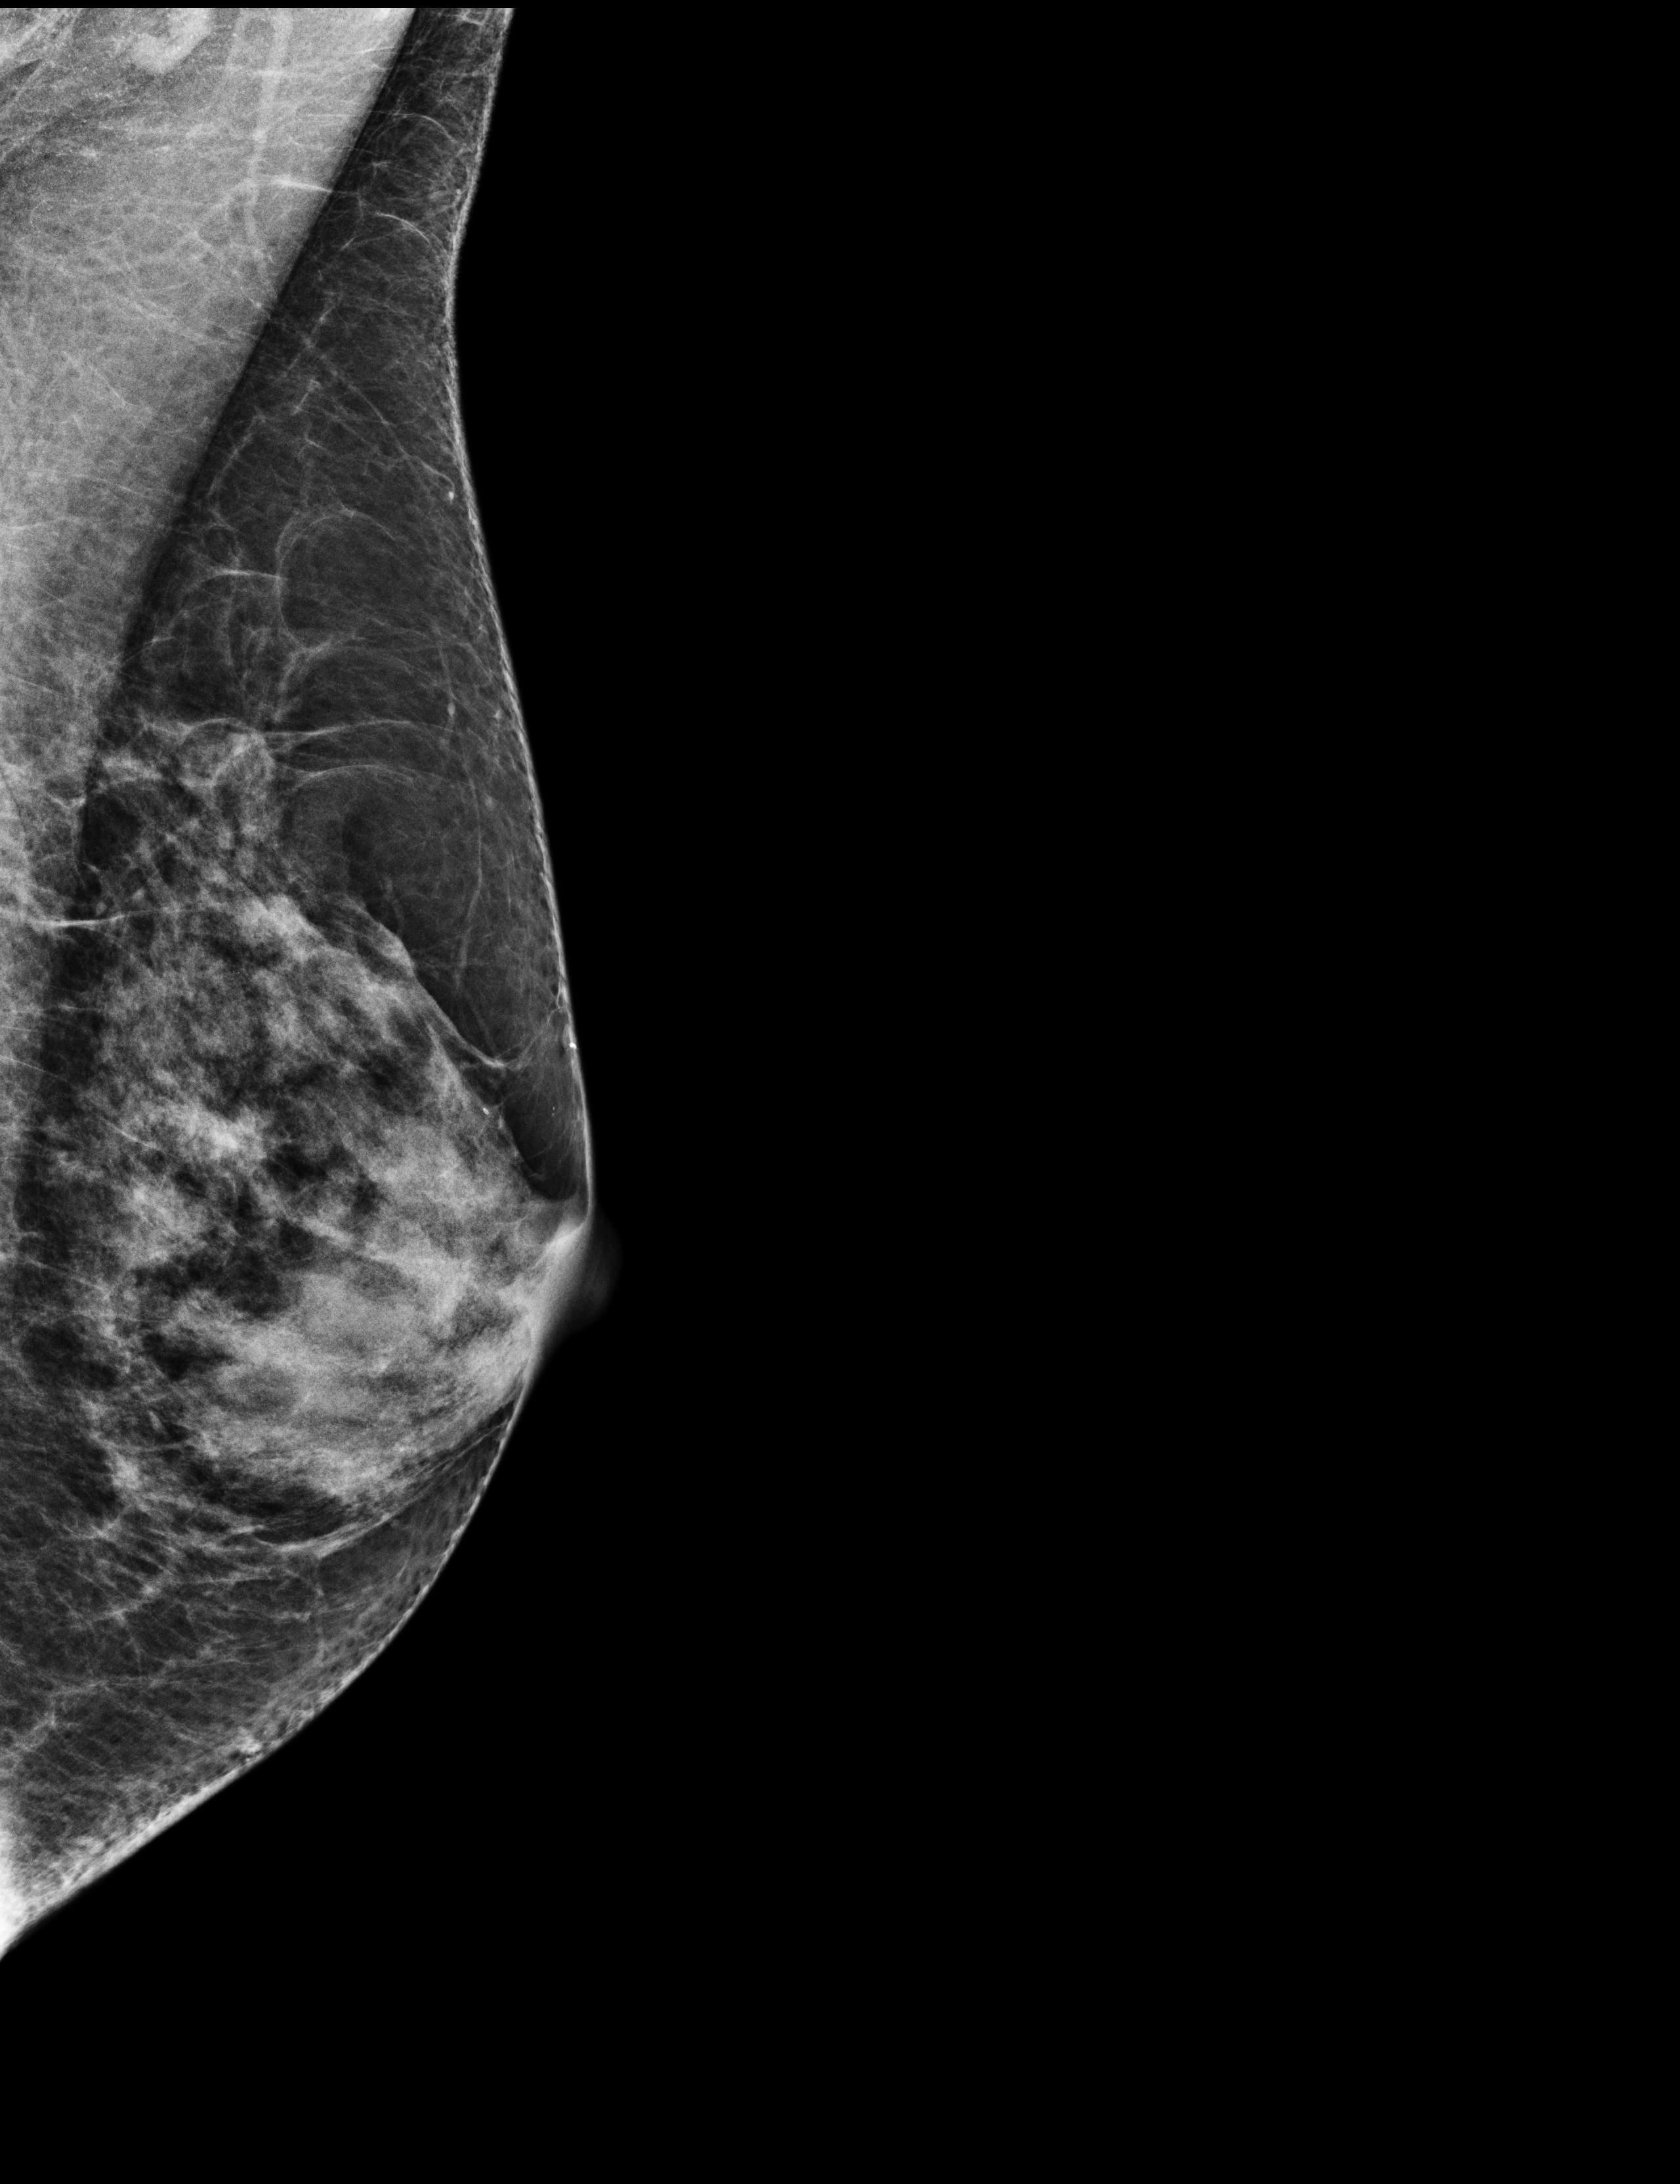
Digital mammogram (FFDM), left breast, MLO view, screening examination, system: Selenia Dimensions. Female patient, age 59 years.
BI-RADS breast density category at the screening exam (both breasts, scale 1–4): 3. Final BI-RADS category for the screening round (tomosynthesis exam, both breasts): category 1. Recall: no recall after this screen.